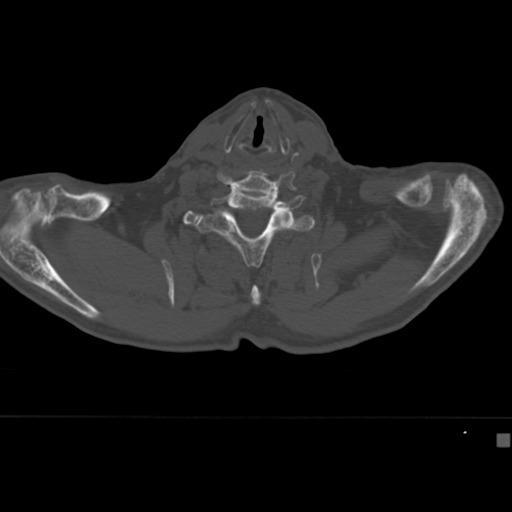
CT including the spine, one axial slice. Position 355 of 430 along the scan axis. 120 kVp. Bone window (W 1800 / L 400 HU). 1.5 mm slice thickness. 512 × 512 image matrix. Patient: male, 64 years. From the clinical record (not read from this slice): primary cancer: uterus; vertebrae with lytic lesions (as recorded): T1, T4, T5, T7, L5.
Structures marked on this image (semi-automatically segmented with operator editing):
- T2 vertebra: bounding box (x1, y1, x2, y2) in pixels: (199, 249, 261, 306)